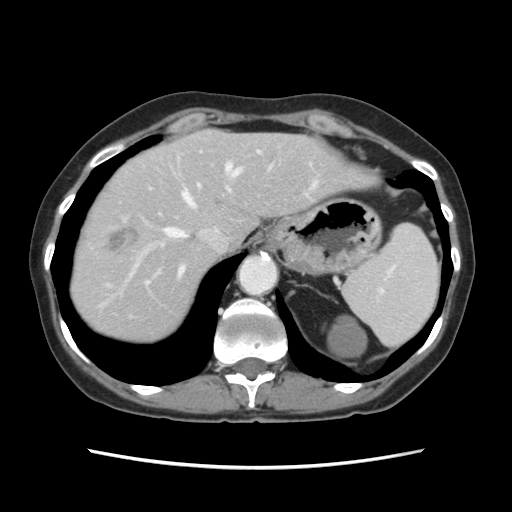
Contrast-enhanced abdominal CT, one axial slice. Slice 95 of 120 in the series (ordered by position). 120 kVp. Intravenous contrast given. Soft-tissue window (W 400 / L 40 HU). 2.5 mm slice thickness. 512 × 512 image matrix, field of view 330 × 330 mm. Female patient, age 70 years. Case-level facts recorded for this patient, not image findings: diagnosis: colorectal cancer liver metastases, imaged before liver resection; multiple liver metastases: no; largest metastasis: 2.5 cm; disease in both lobes: no.
Outlined on this slice (manually delineated by an expert):
- hepatic veins: bounding box [x1, y1, x2, y2] px = [127, 164, 240, 281]
- liver: [72, 130, 367, 344]
- planned liver remnant (the part of the liver to remain after resection): [137, 130, 365, 275]
- portal vein (with intrahepatic branches): [145, 150, 261, 285]
- liver metastasis: [110, 228, 139, 250]